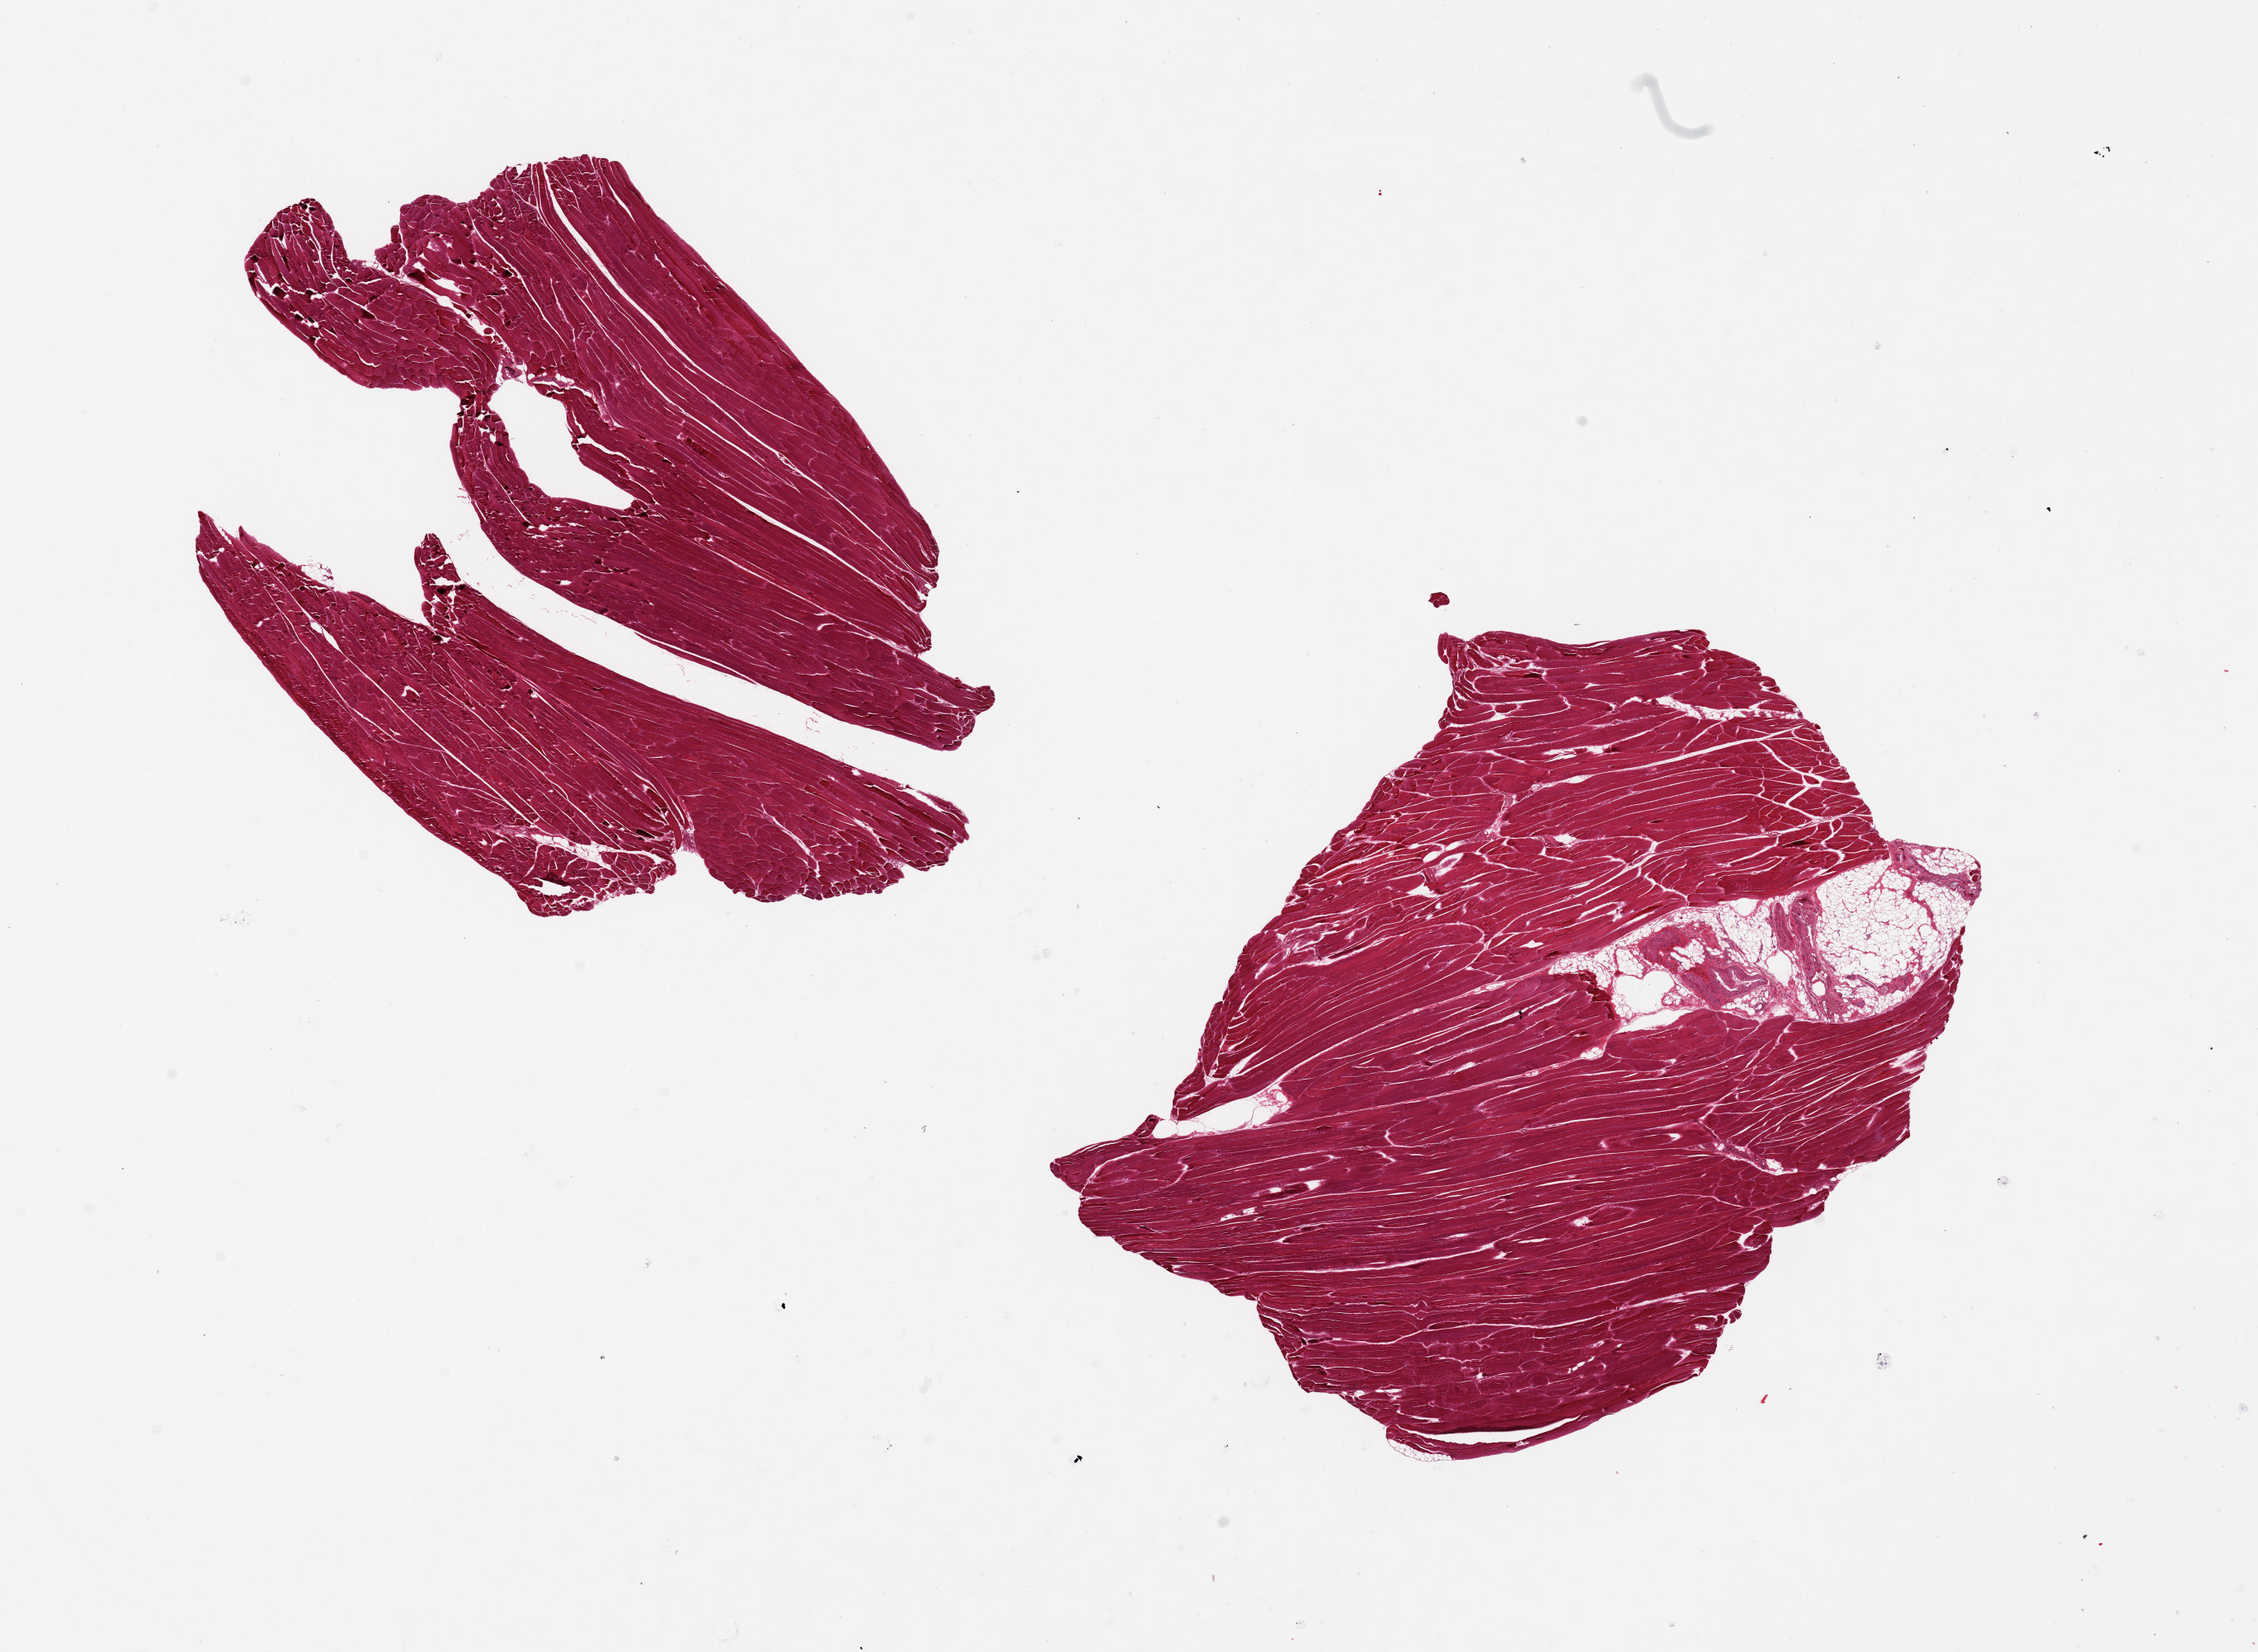
Digitized hematoxylin and eosin (H&E)-stained section — a low-resolution overview of the entire scanned area, about 21.7 x 15.8 mm. PAXgene-fixed, paraffin-embedded tissue. Sampled site (target tissue): skeletal muscle. Tissue donor sample.
- pathologist's review note for this sample: 2 pieces; 9x6 & 8x7mm; focal adipose tissue (~5% tissue)